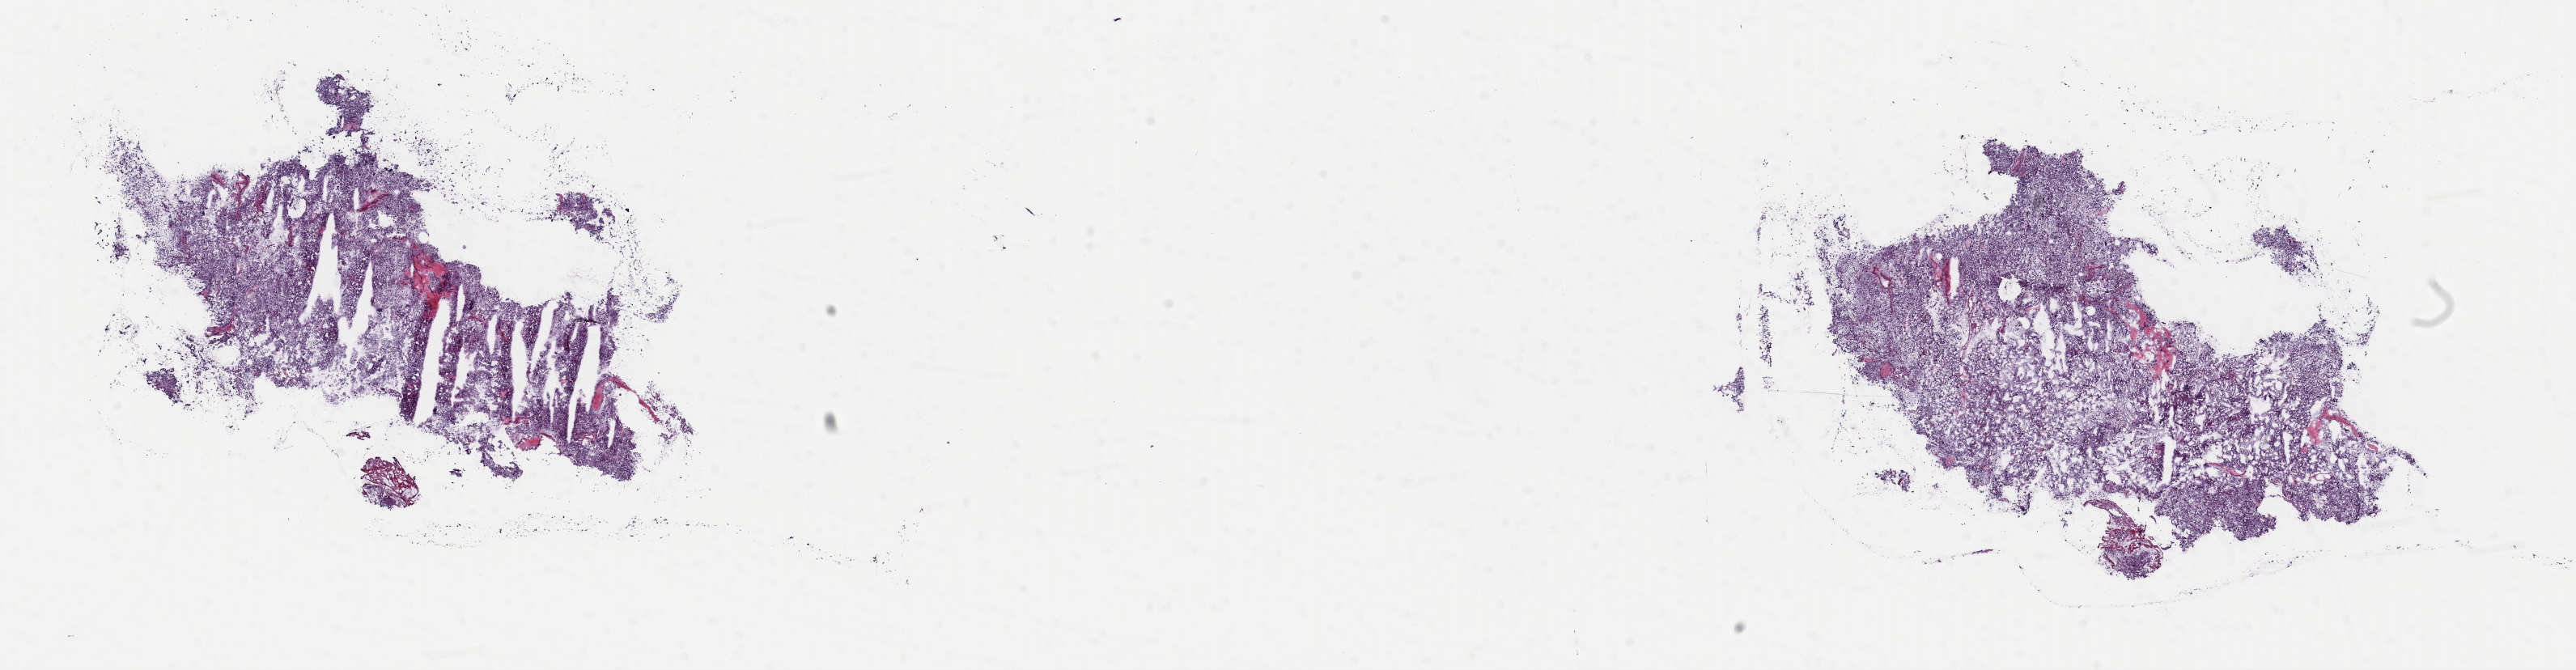
H&E whole-slide image, shown as a low-resolution overview of the whole scanned area (about 25.1 x 6.5 mm). Frozen section. Primary tumour sample from the adrenal gland. Patient: female, age at initial diagnosis 62 years. Slide review estimates, as recorded: tumour cells 90%, tumour nuclei 90%, normal cells 0%, stromal cells 5%, necrosis 5%. Infiltration values recorded for this section: lymphocyte infiltration 0%, monocyte infiltration 0%, neutrophil infiltration 0%.
* laterality: left
* histologic diagnosis: Pheochromocytoma, malignant